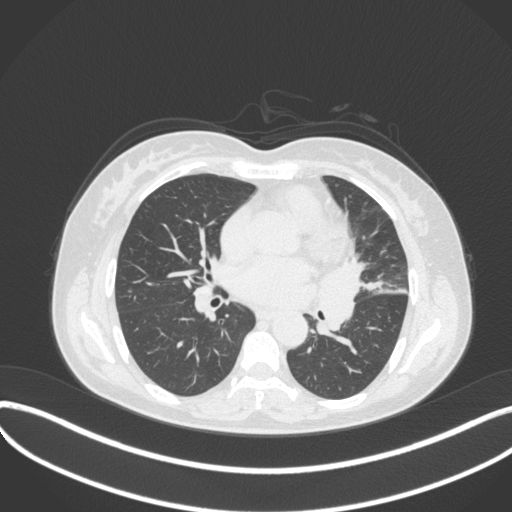
Chest CT, one axial slice; position 176 of 373 along the scan axis; 120 kVp; lung window (W 1500 / L -600 HU); 1 mm slice thickness; 512 × 512 image matrix, field of view 400 × 400 mm. Female patient, age 54 years. Case-level facts recorded for this patient, not image findings: clinical TNM (as recorded): T2a N1 M0; histopathological grade: G3.
Outlined on this slice (bounding box drawn by a radiologist):
- lung tumour (recorded histology: small cell carcinoma): box from (x=312, y=257) to (x=368, y=339) px